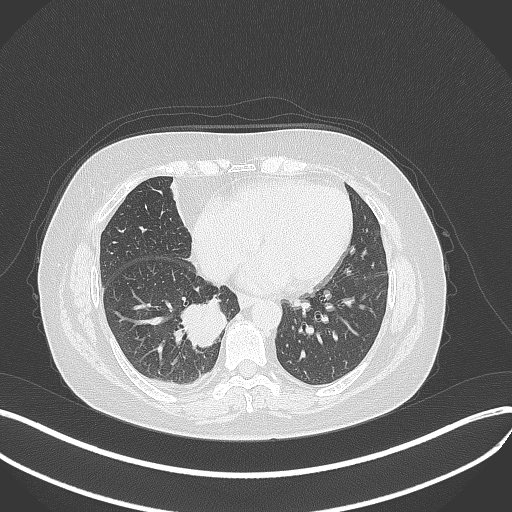
Chest CT, one axial slice. Slice 132 of 381 in the series (ordered by position). Reconstruction kernel B70f. Lung window (W 1500 / L -600 HU). 512 × 512 image matrix, field of view 400 × 400 mm. Female patient, age 56 years. Case-level facts recorded for this patient, not image findings: clinical TNM (as recorded): T2b N1 M0.
Annotated regions visible in this slice (bounding box drawn by a radiologist):
- lung tumour (recorded histology: small cell carcinoma): box from (x=178, y=296) to (x=233, y=350) px